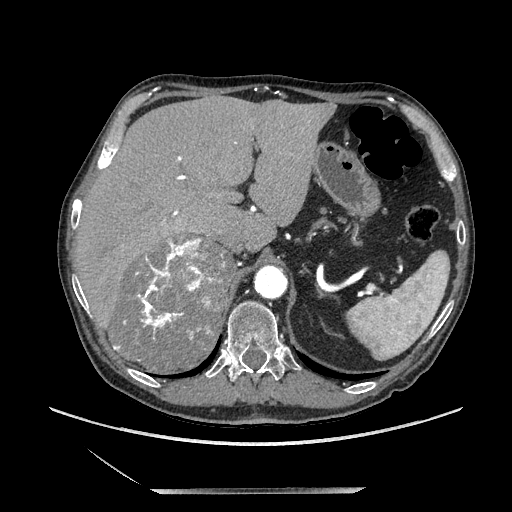
Contrast-enhanced abdominal CT, one axial slice; slice 153 of 243 in the series (ordered by position); soft-tissue window (W 400 / L 40 HU); 1.25 mm slice thickness; 512 × 512 image matrix, field of view 420 × 420 mm. Male patient. From the clinical record (not read from this slice): diagnosis: adrenocortical carcinoma; tumour side: right adrenal.
Outlined on this slice (semi-automatic segmentation, software-assisted and operator-edited):
- mass: box from (x=113, y=235) to (x=233, y=374) px